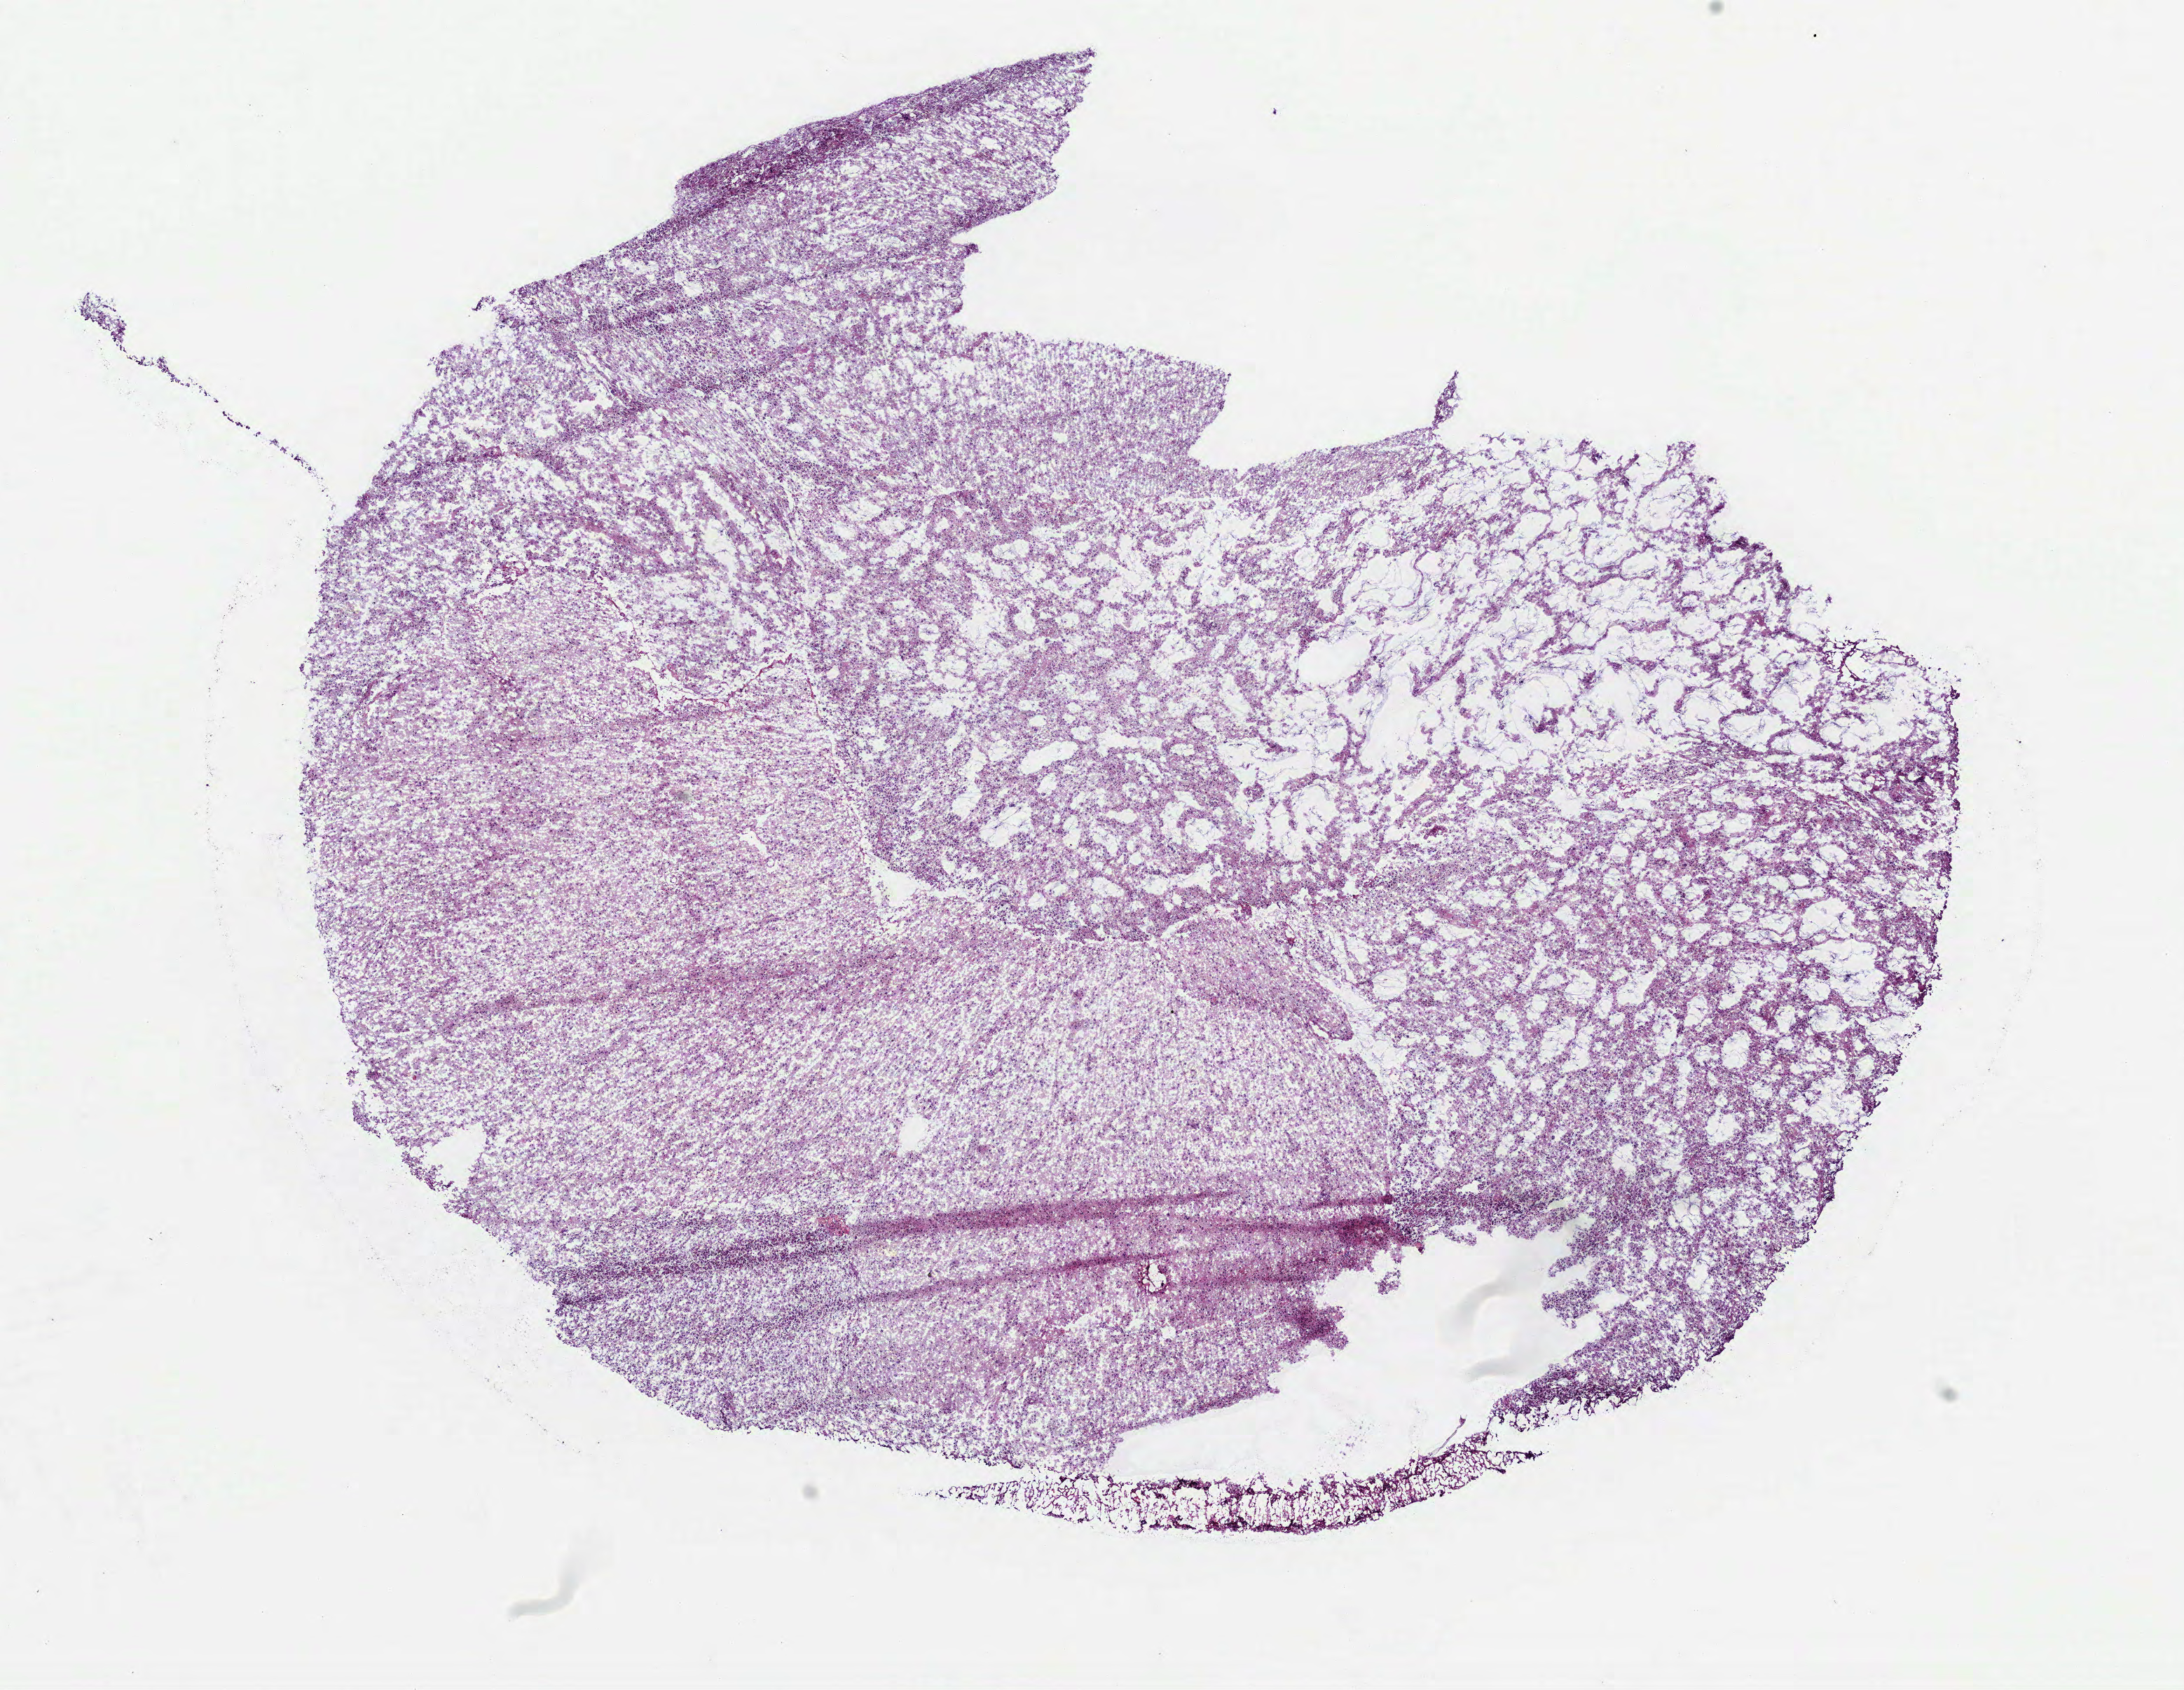
Whole-slide histology image, H&E-stained, shown as a low-resolution overview of the whole scanned area (about 12.6 x 9.7 mm, acquisition: 40x scan). Frozen section. Sample: primary tumour, brain. Female patient; age at initial diagnosis 41 years. Histologic grade: G2 (moderately differentiated). Slide review estimates, as recorded: tumour cells 100%, tumour nuclei 75%, normal cells 0%, stromal cells 0%, necrosis 0%.
Laterality: right. Diagnosis: Oligodendroglioma, NOS (cerebrum).